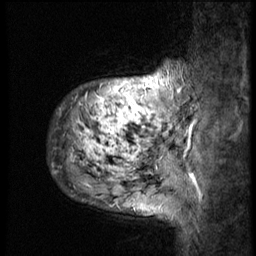
Breast MRI (dynamic contrast-enhanced), one sagittal slice; position 8 of 58 along the scan axis; 3 images stored at this slice position (order not interpretable as contrast timing); 1.5 T; TE 4.2 ms, TR 9 ms; 2.5 mm slice thickness; 256 × 256 image matrix. Female patient, age 50 years. Case-level facts recorded for this patient, not image findings: setting: breast cancer imaged before/during neoadjuvant chemotherapy; receptor status: triple-negative.
Structures marked on this image (semi-automatically segmented with operator editing):
- analysis volume of interest (the breast-tissue region the enhancement analysis was run in; not a lesion): box from (x=49, y=52) to (x=186, y=214) px
- tumour enhancement mask (voxels above the 140 % enhancement threshold inside the analysis volume of interest): (x=57, y=88)–(x=182, y=180)